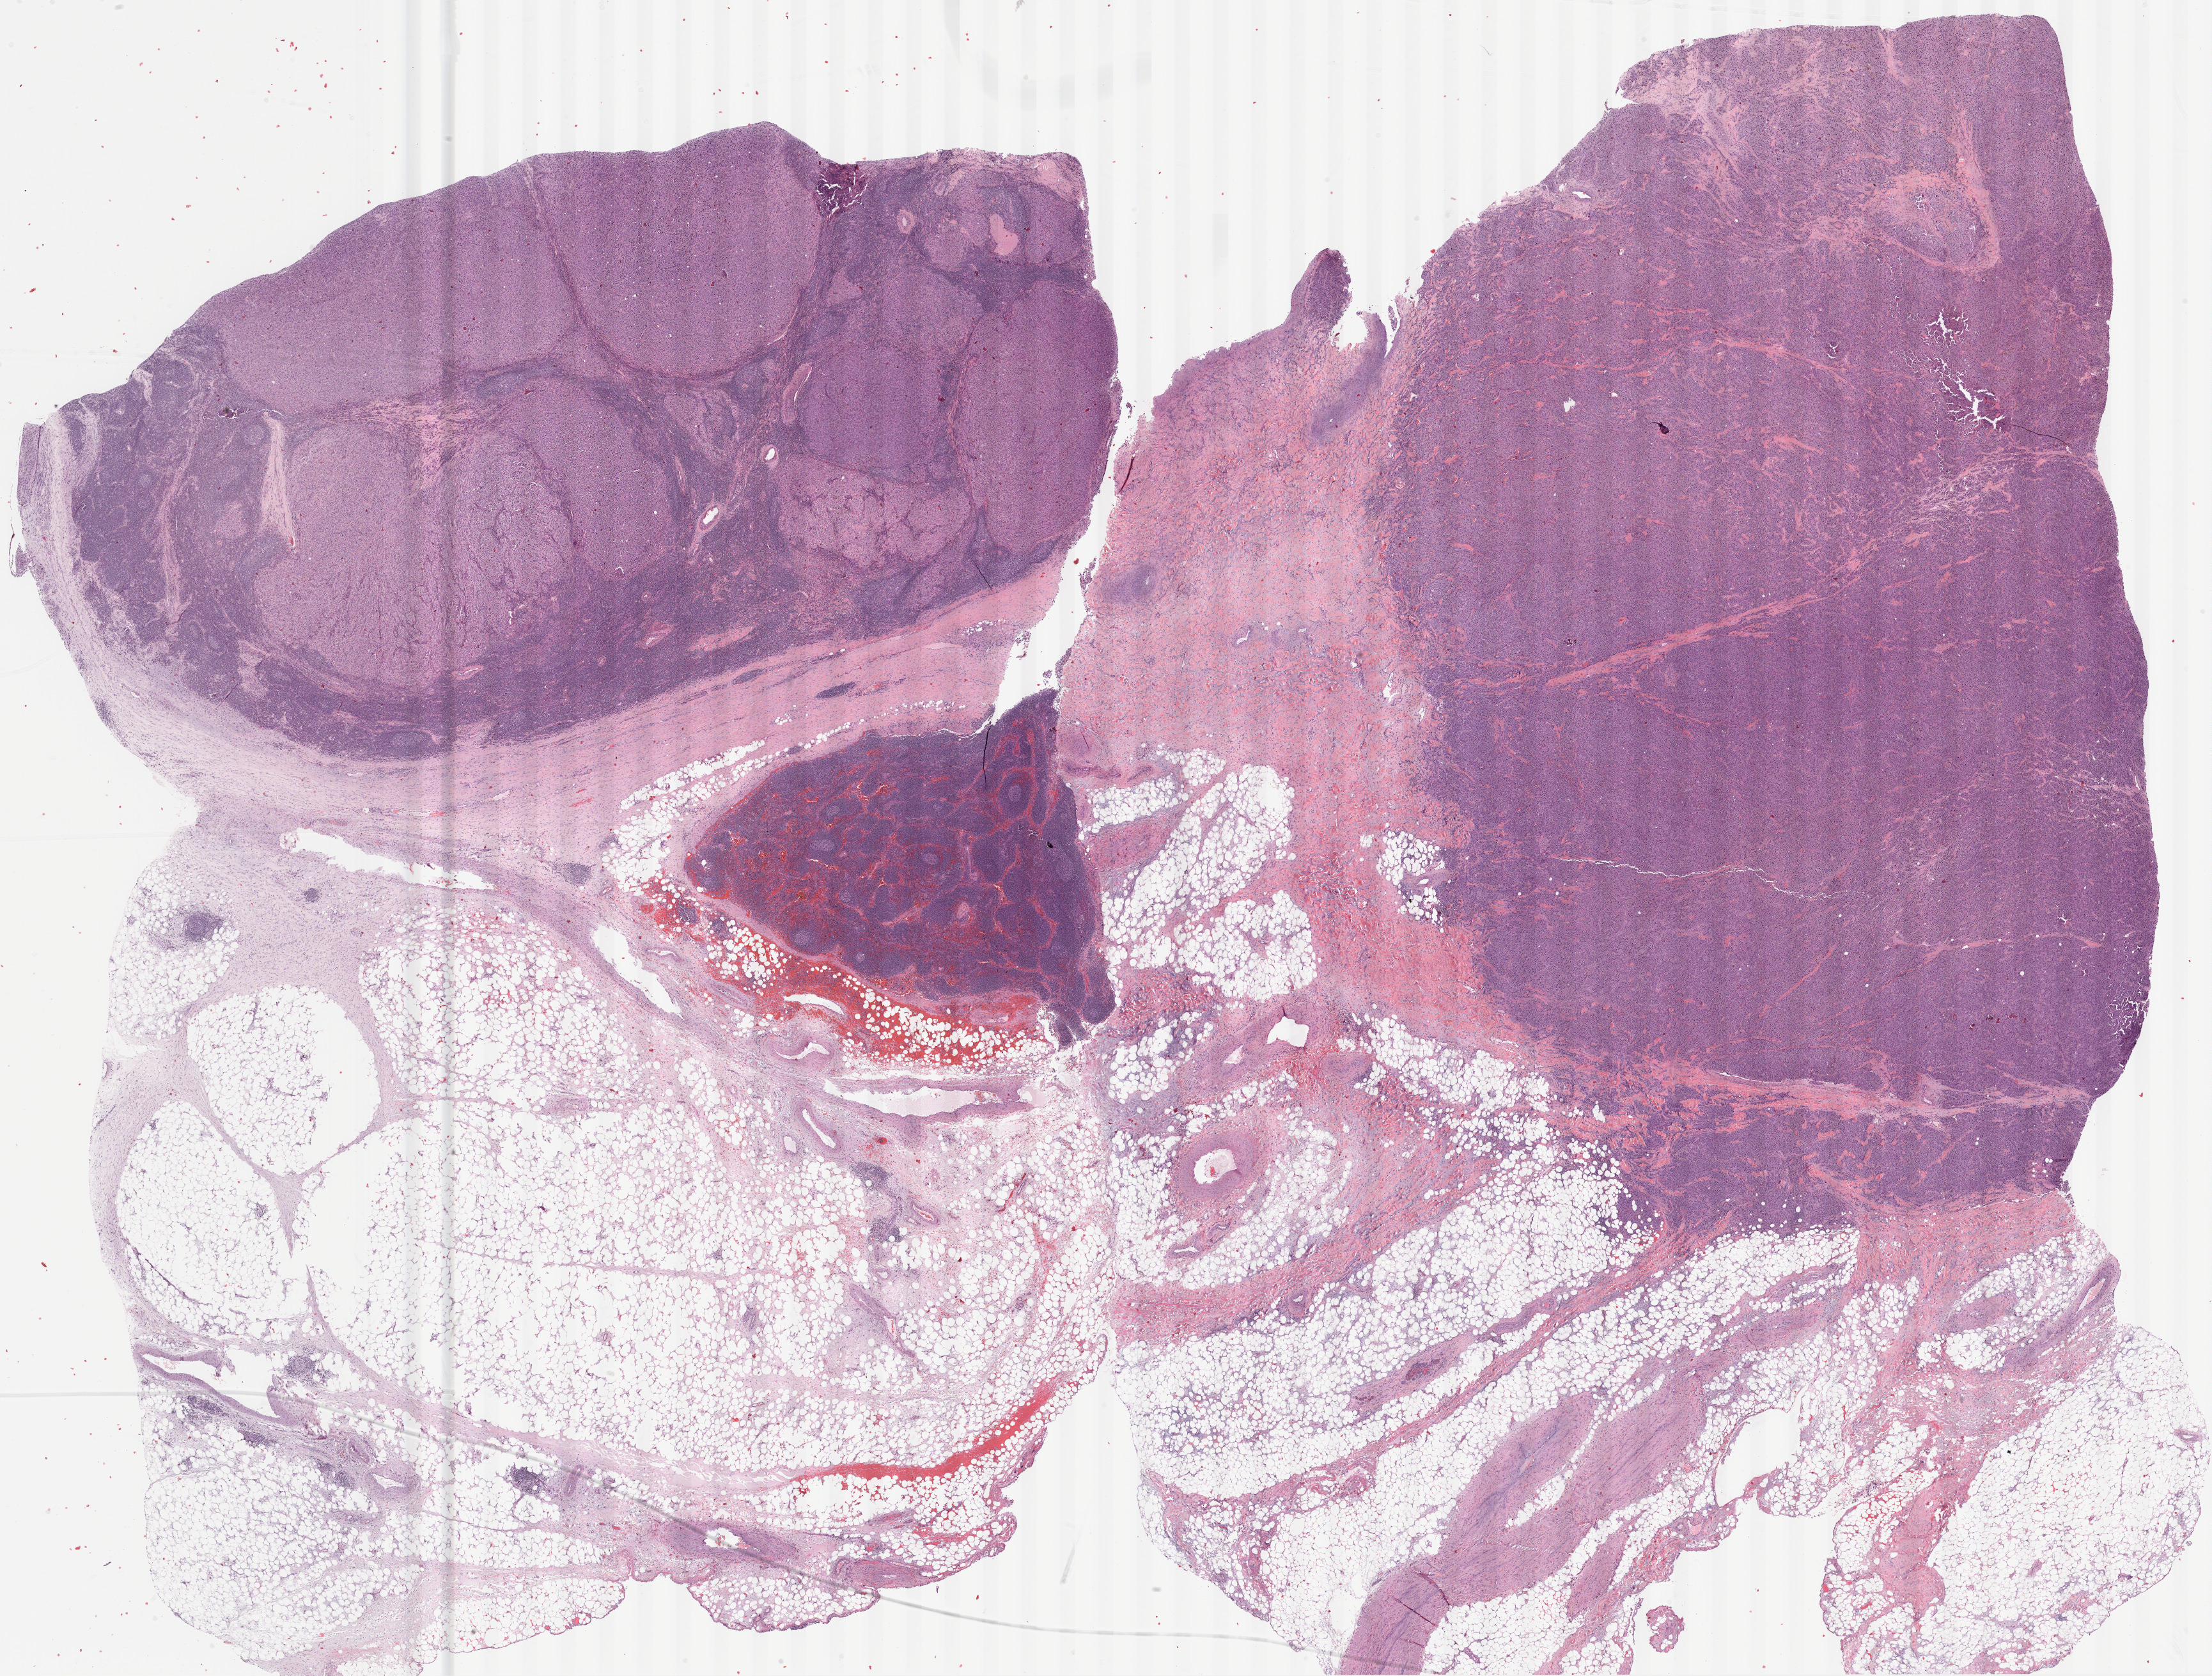
Whole-slide histology image, H&E, a low-resolution overview of the entire scanned area, about 27.9 x 21.1 mm, formalin-fixed paraffin-embedded (FFPE) diagnostic section, metastatic tumour sample, sampled site not recorded. Female patient; age at initial diagnosis 30 years.
This section: metastatic tumour tissue. Patient diagnosis: Malignant melanoma, NOS.